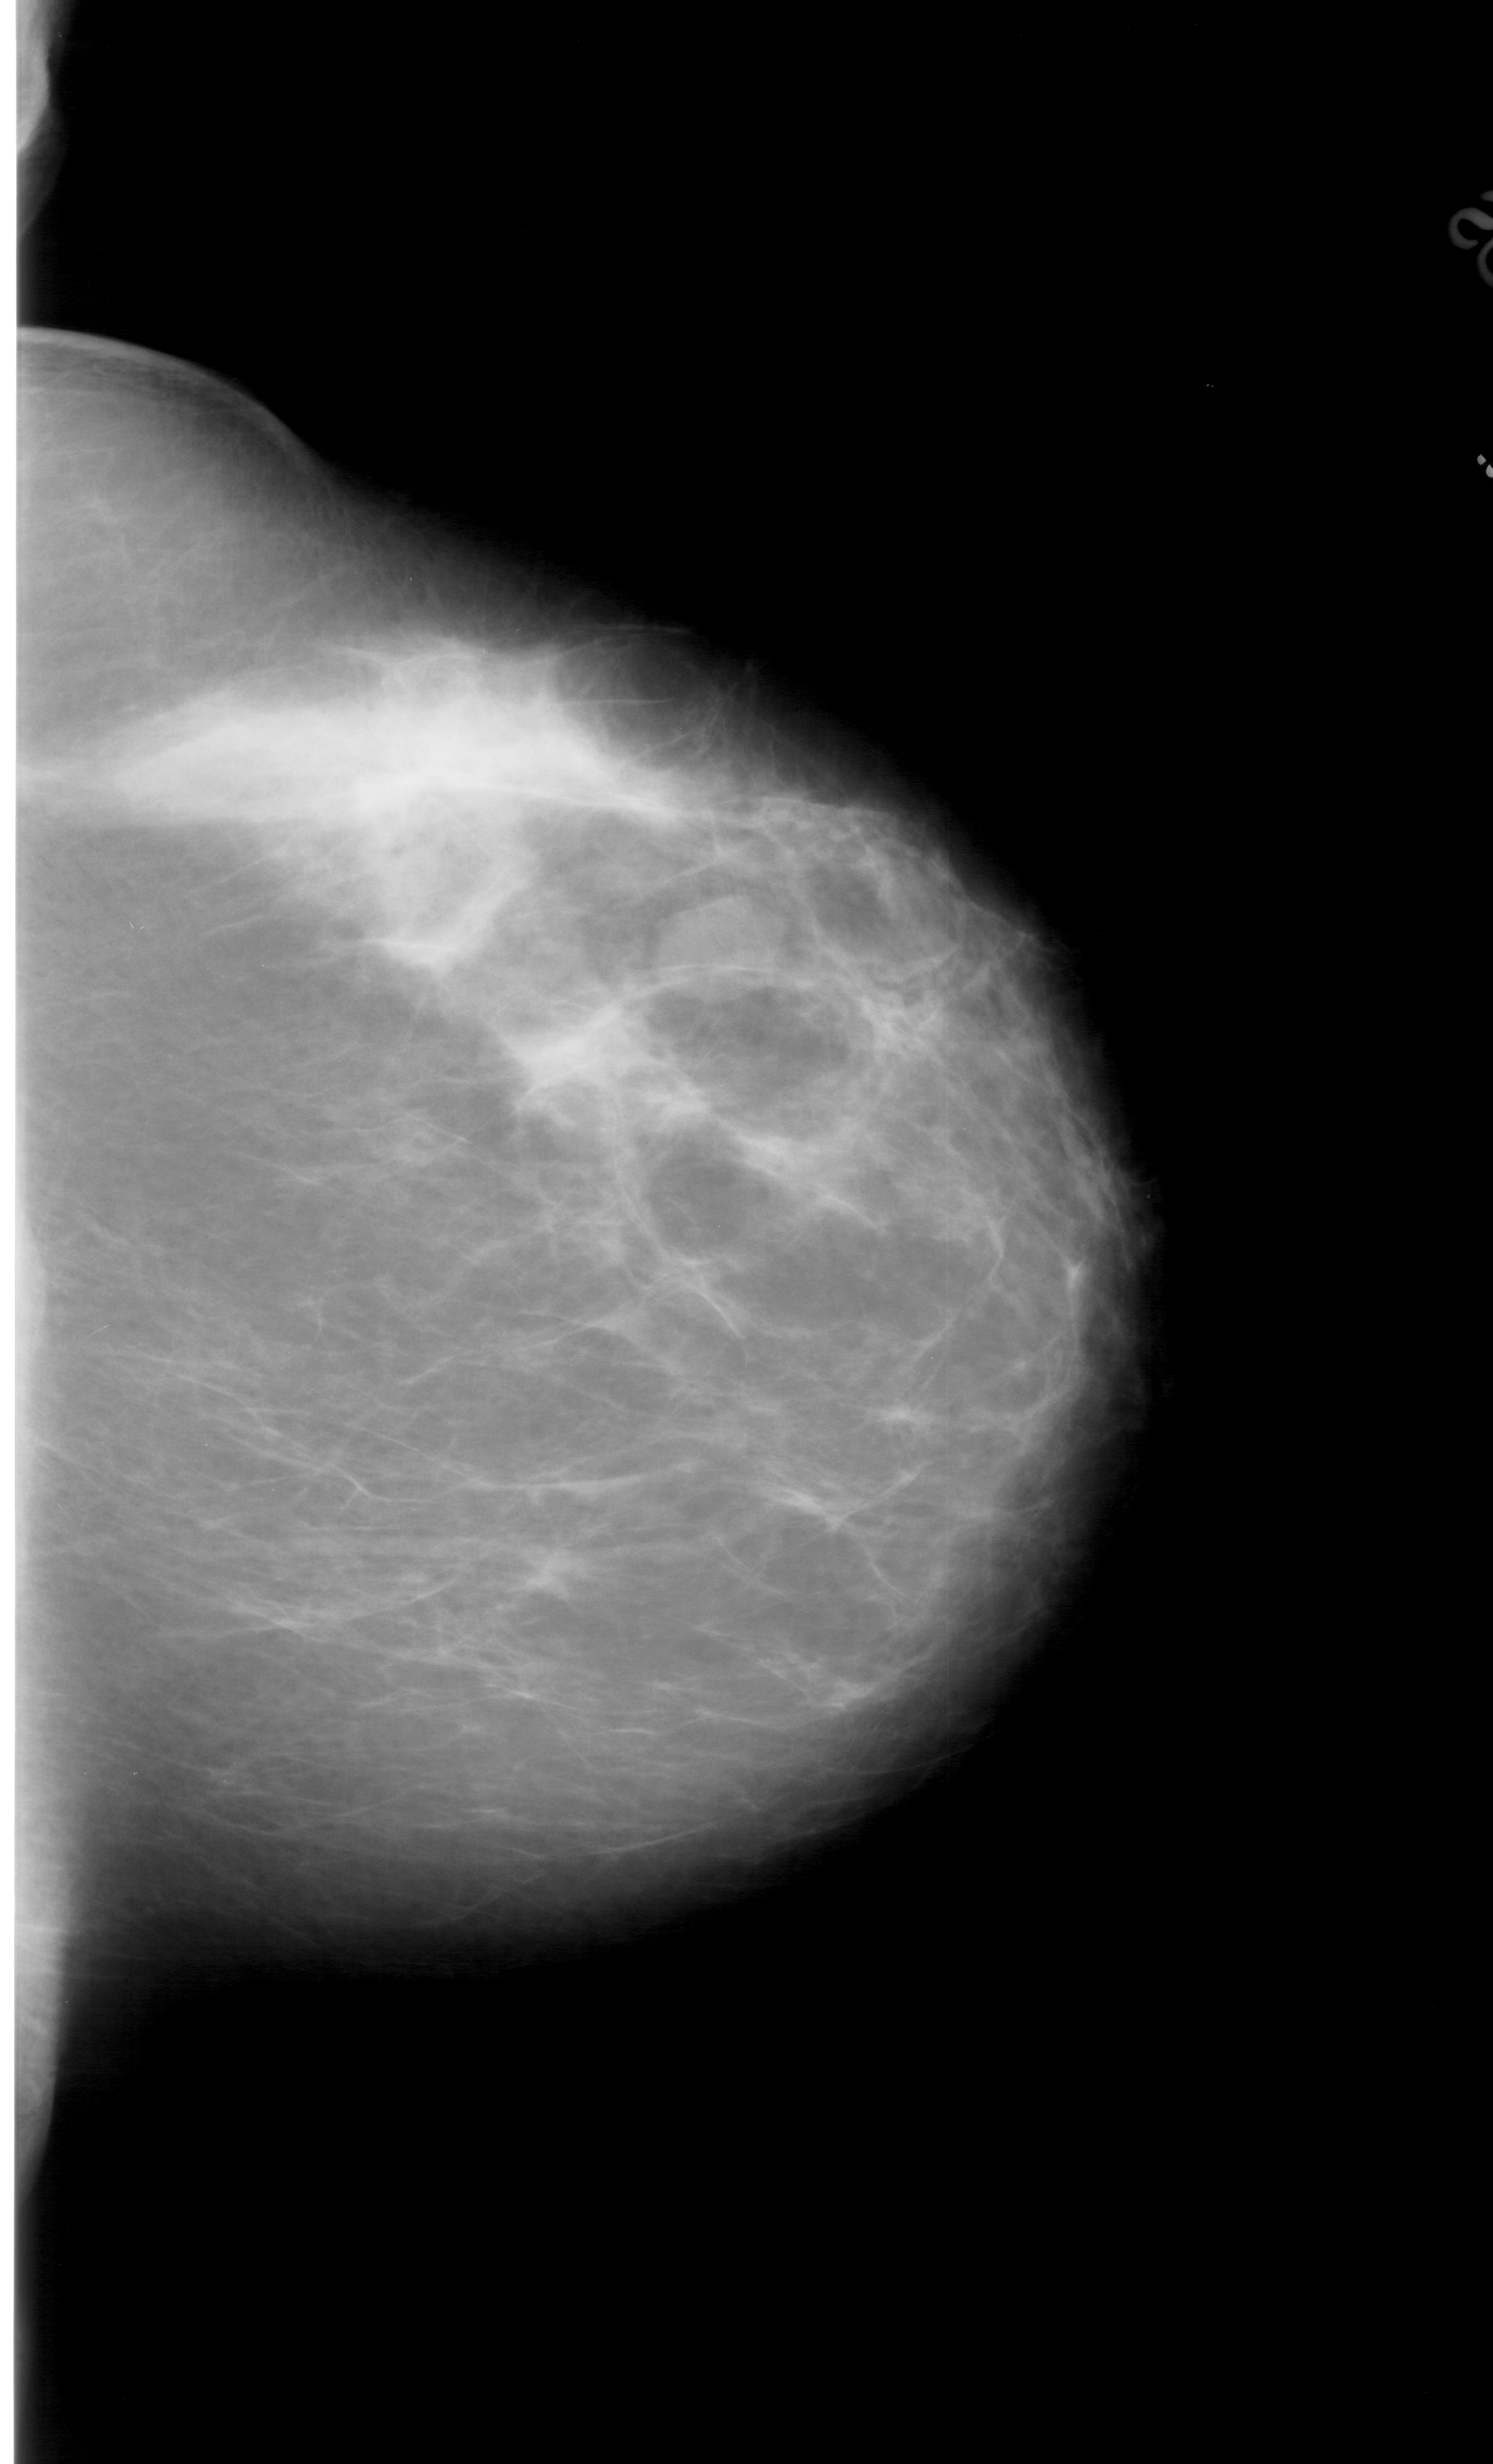
Mammogram (digitized film). Right breast. CC view. Breast composition: scattered fibroglandular densities (BI-RADS density category 2 of 4). 1493 × 2464 image matrix.
Marked abnormalities (boxes around the expert regions of interest):
- mass, shape oval, margins circumscribed; BI-RADS assessment category 3; pathology result (as recorded, not read from the image): benign: box from (x=635, y=883) to (x=796, y=1012) px